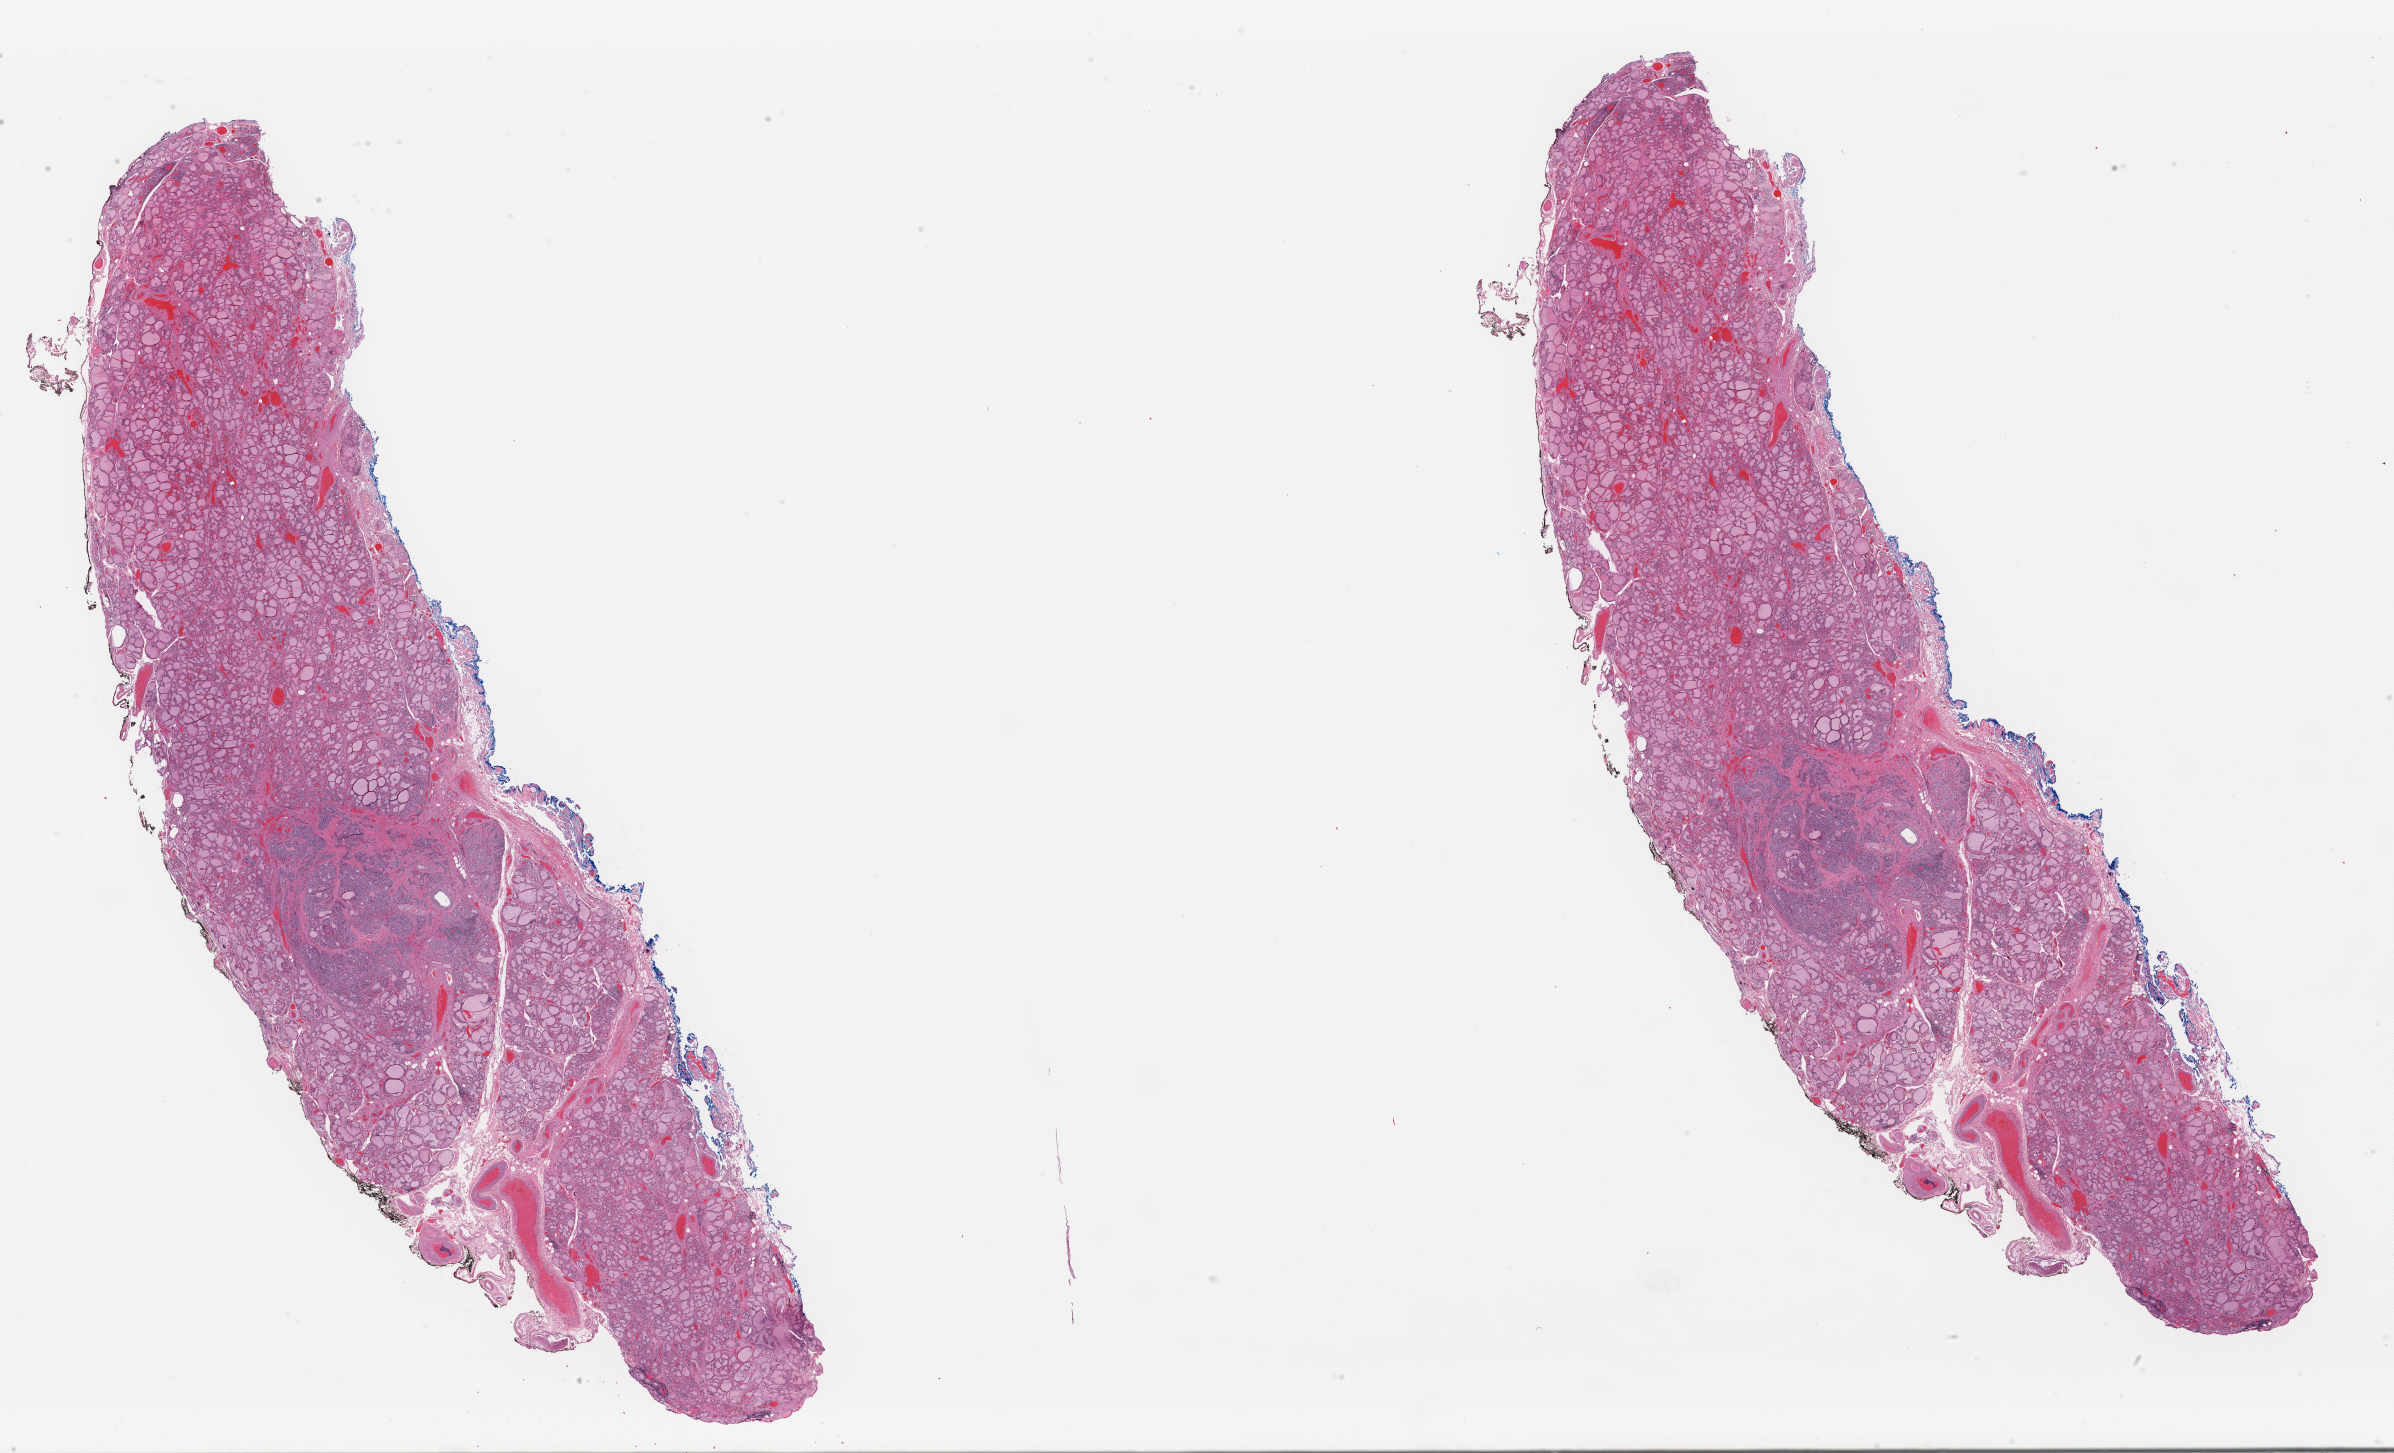
H&E whole-slide image, a low-resolution overview of the entire scanned area, about 37.8 x 22.9 mm; formalin-fixed paraffin-embedded (FFPE) diagnostic section; primary tumour sample from the thyroid. Patient: female, age at initial diagnosis 46 years.
Diagnosis: Papillary adenocarcinoma, NOS. TNM: T1 N0 M0. Lymph nodes positive (case pathology): 0 of 3 examined. AJCC pathologic stage: I (7th edition).